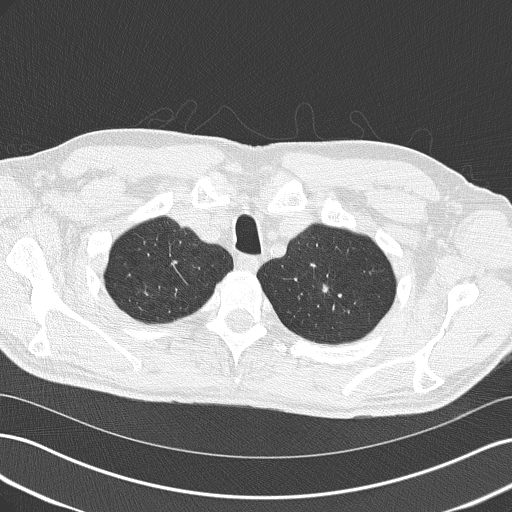
Axial slice from a low-dose chest CT screening exam. Second annual screen. Lung window (W 1500 / L -600 HU). Lung (sharp) reconstruction kernel (B50f). 140 kVp. Slice 35 of 185 in the series. 512 × 512 image matrix. Male participant, aged 64 years at enrolment. Former smoker at enrolment.
Lesion marked by an expert reader, box from (x=296, y=277) to (x=342, y=313) px. The screening reader recorded 2 non-calcified nodules or masses ≥4 mm on this exam (left upper lobe, left upper lobe); which of them this box marks is not recorded. Later outcome: lung cancer diagnosed 482 days after this screen (after the third annual screen) — adenocarcinoma, NOS, left upper lobe, poorly differentiated (G3), stage IA (AJCC 6th edition), 10 mm at pathology.